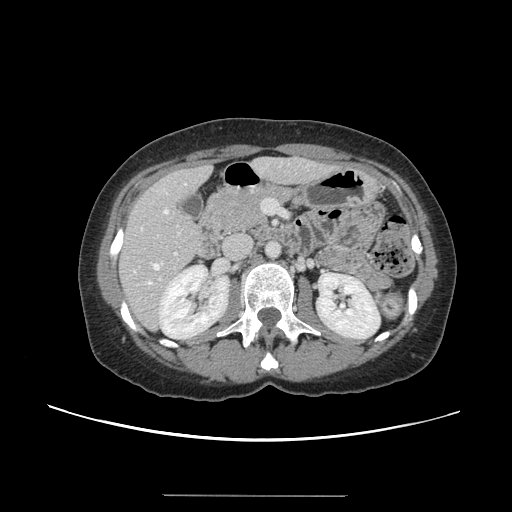
Contrast-enhanced abdominal CT, one axial slice; slice 63 of 144 in the series (ordered by position); soft-tissue window (W 400 / L 40 HU); 2.5 mm slice thickness; 512 × 512 image matrix, field of view 380 × 380 mm. Female patient, age 53 years. Case-level facts recorded for this patient, not image findings: diagnosis: colorectal cancer liver metastases, imaged before liver resection; multiple liver metastases: yes; largest metastasis: 1.1 cm; disease in both lobes: no.
Outlined on this slice (outlined manually by an expert reader):
- hepatic veins: bounding box [x1, y1, x2, y2] px = [149, 184, 186, 284]
- liver: [121, 159, 332, 329]
- planned liver remnant (the part of the liver to remain after resection): [121, 159, 326, 308]
- portal vein (with intrahepatic branches): [159, 252, 178, 281]